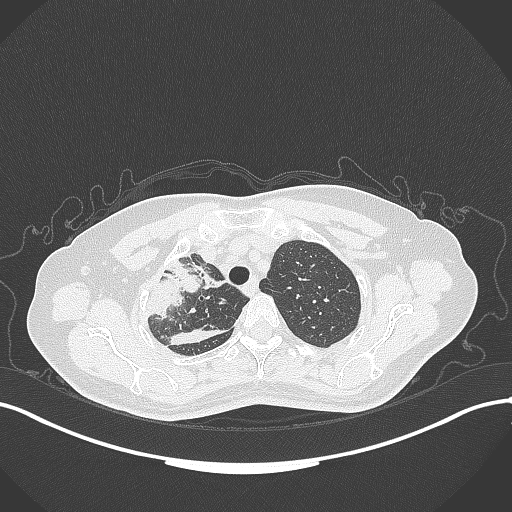
Chest CT, one axial slice. Position 262 of 309 along the scan axis. Reconstruction kernel B70f. Lung window (W 1500 / L -600 HU). 1 mm slice thickness. 512 × 512 image matrix, field of view 400 × 400 mm. Patient: female, 60 years. Case-level facts recorded for this patient, not image findings: clinical TNM (as recorded): T3 N1 M1.
Annotated regions visible in this slice (bounding box drawn by a radiologist):
- lung tumour (recorded histology: adenocarcinoma): bounding box [x1, y1, x2, y2] px = [135, 258, 229, 320]